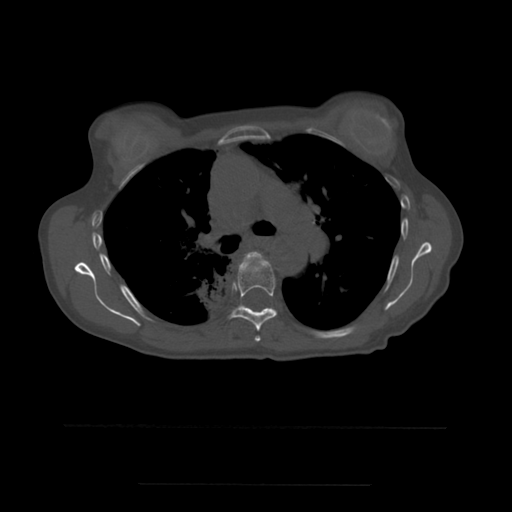
CT including the spine, one axial slice. Slice 377 of 544 in the series (ordered by position). Bone window (W 1800 / L 400 HU). 1.25 mm slice thickness. 512 × 512 image matrix, field of view 350 × 350 mm. Patient age 58 years. Case-level facts recorded for this patient, not image findings: primary cancer: lung.
Annotated regions visible in this slice (semi-automatic segmentation, software-assisted and operator-edited):
- T5 vertebra: bounding box [x1, y1, x2, y2] px = [245, 252, 262, 342]
- T6 vertebra: [223, 256, 277, 332]